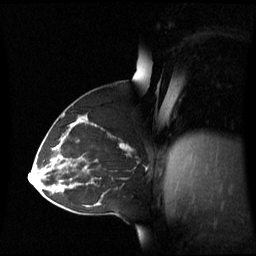
Breast MRI (dynamic contrast-enhanced), one sagittal slice; position 34 of 60 along the scan axis; dynamic contrast-enhanced series, image 2 of 3 at this slice position (ordered by acquisition); 1.5 T; TE 4.2 ms, TR 8.4 ms; 2.8 mm slice thickness; 256 × 256 image matrix, field of view 270 × 270 mm. Female patient, age 43 years. From the clinical record (not read from this slice): setting: breast cancer imaged before/during neoadjuvant chemotherapy; receptor status: triple-negative.
Structures marked on this image (semi-automatic segmentation, software-assisted and operator-edited):
- analysis volume of interest (the breast-tissue region the enhancement analysis was run in; not a lesion): bounding box (x1, y1, x2, y2) in pixels: (55, 124, 139, 173)
- tumour enhancement mask (voxels above the 70 % enhancement threshold inside the analysis volume of interest): (120, 143, 129, 148)